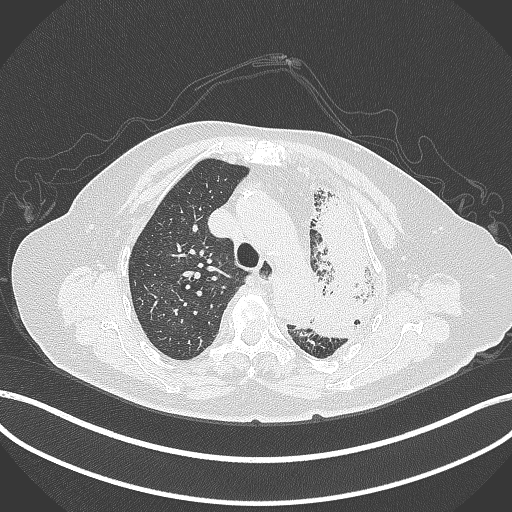
Chest CT, one axial slice. 120 kVp. Lung window (W 1500 / L -600 HU). 1 mm slice thickness. 512 × 512 image matrix, field of view 400 × 400 mm. Female patient, age 75 years. Case-level facts recorded for this patient, not image findings: clinical TNM (as recorded): T3 N3 M1.
Structures marked on this image (bounding box drawn by a radiologist):
- lung tumour (recorded histology: adenocarcinoma): bounding box <301,188,377,346> (left, top, right, bottom; pixels)